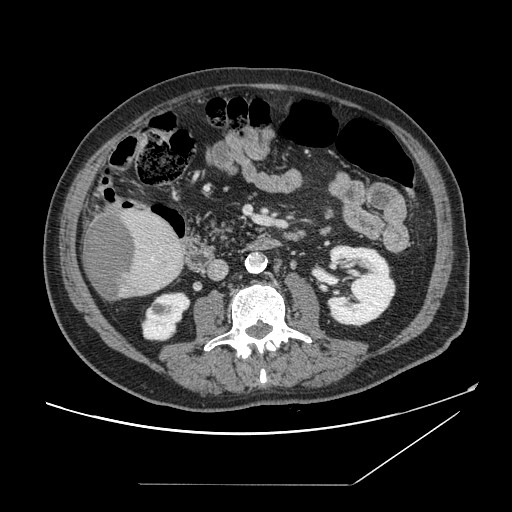
Contrast-enhanced abdominal CT, one axial slice. Slice 46 of 166 in the series (ordered by position). 120 kVp. Intravenous contrast given. Soft-tissue window (W 400 / L 40 HU). 2.5 mm slice thickness. 512 × 512 image matrix, field of view 416 × 416 mm. Male patient, age 80 years. Case-level facts recorded for this patient, not image findings: diagnosis: colorectal cancer liver metastases, imaged before liver resection; multiple liver metastases: no; largest metastasis: 2.2 cm; chemotherapy before resection: no.
Outlined on this slice (expert manual segmentation):
- liver: bounding box <83,206,185,300> (left, top, right, bottom; pixels)
- liver metastasis: <83,213,137,298>